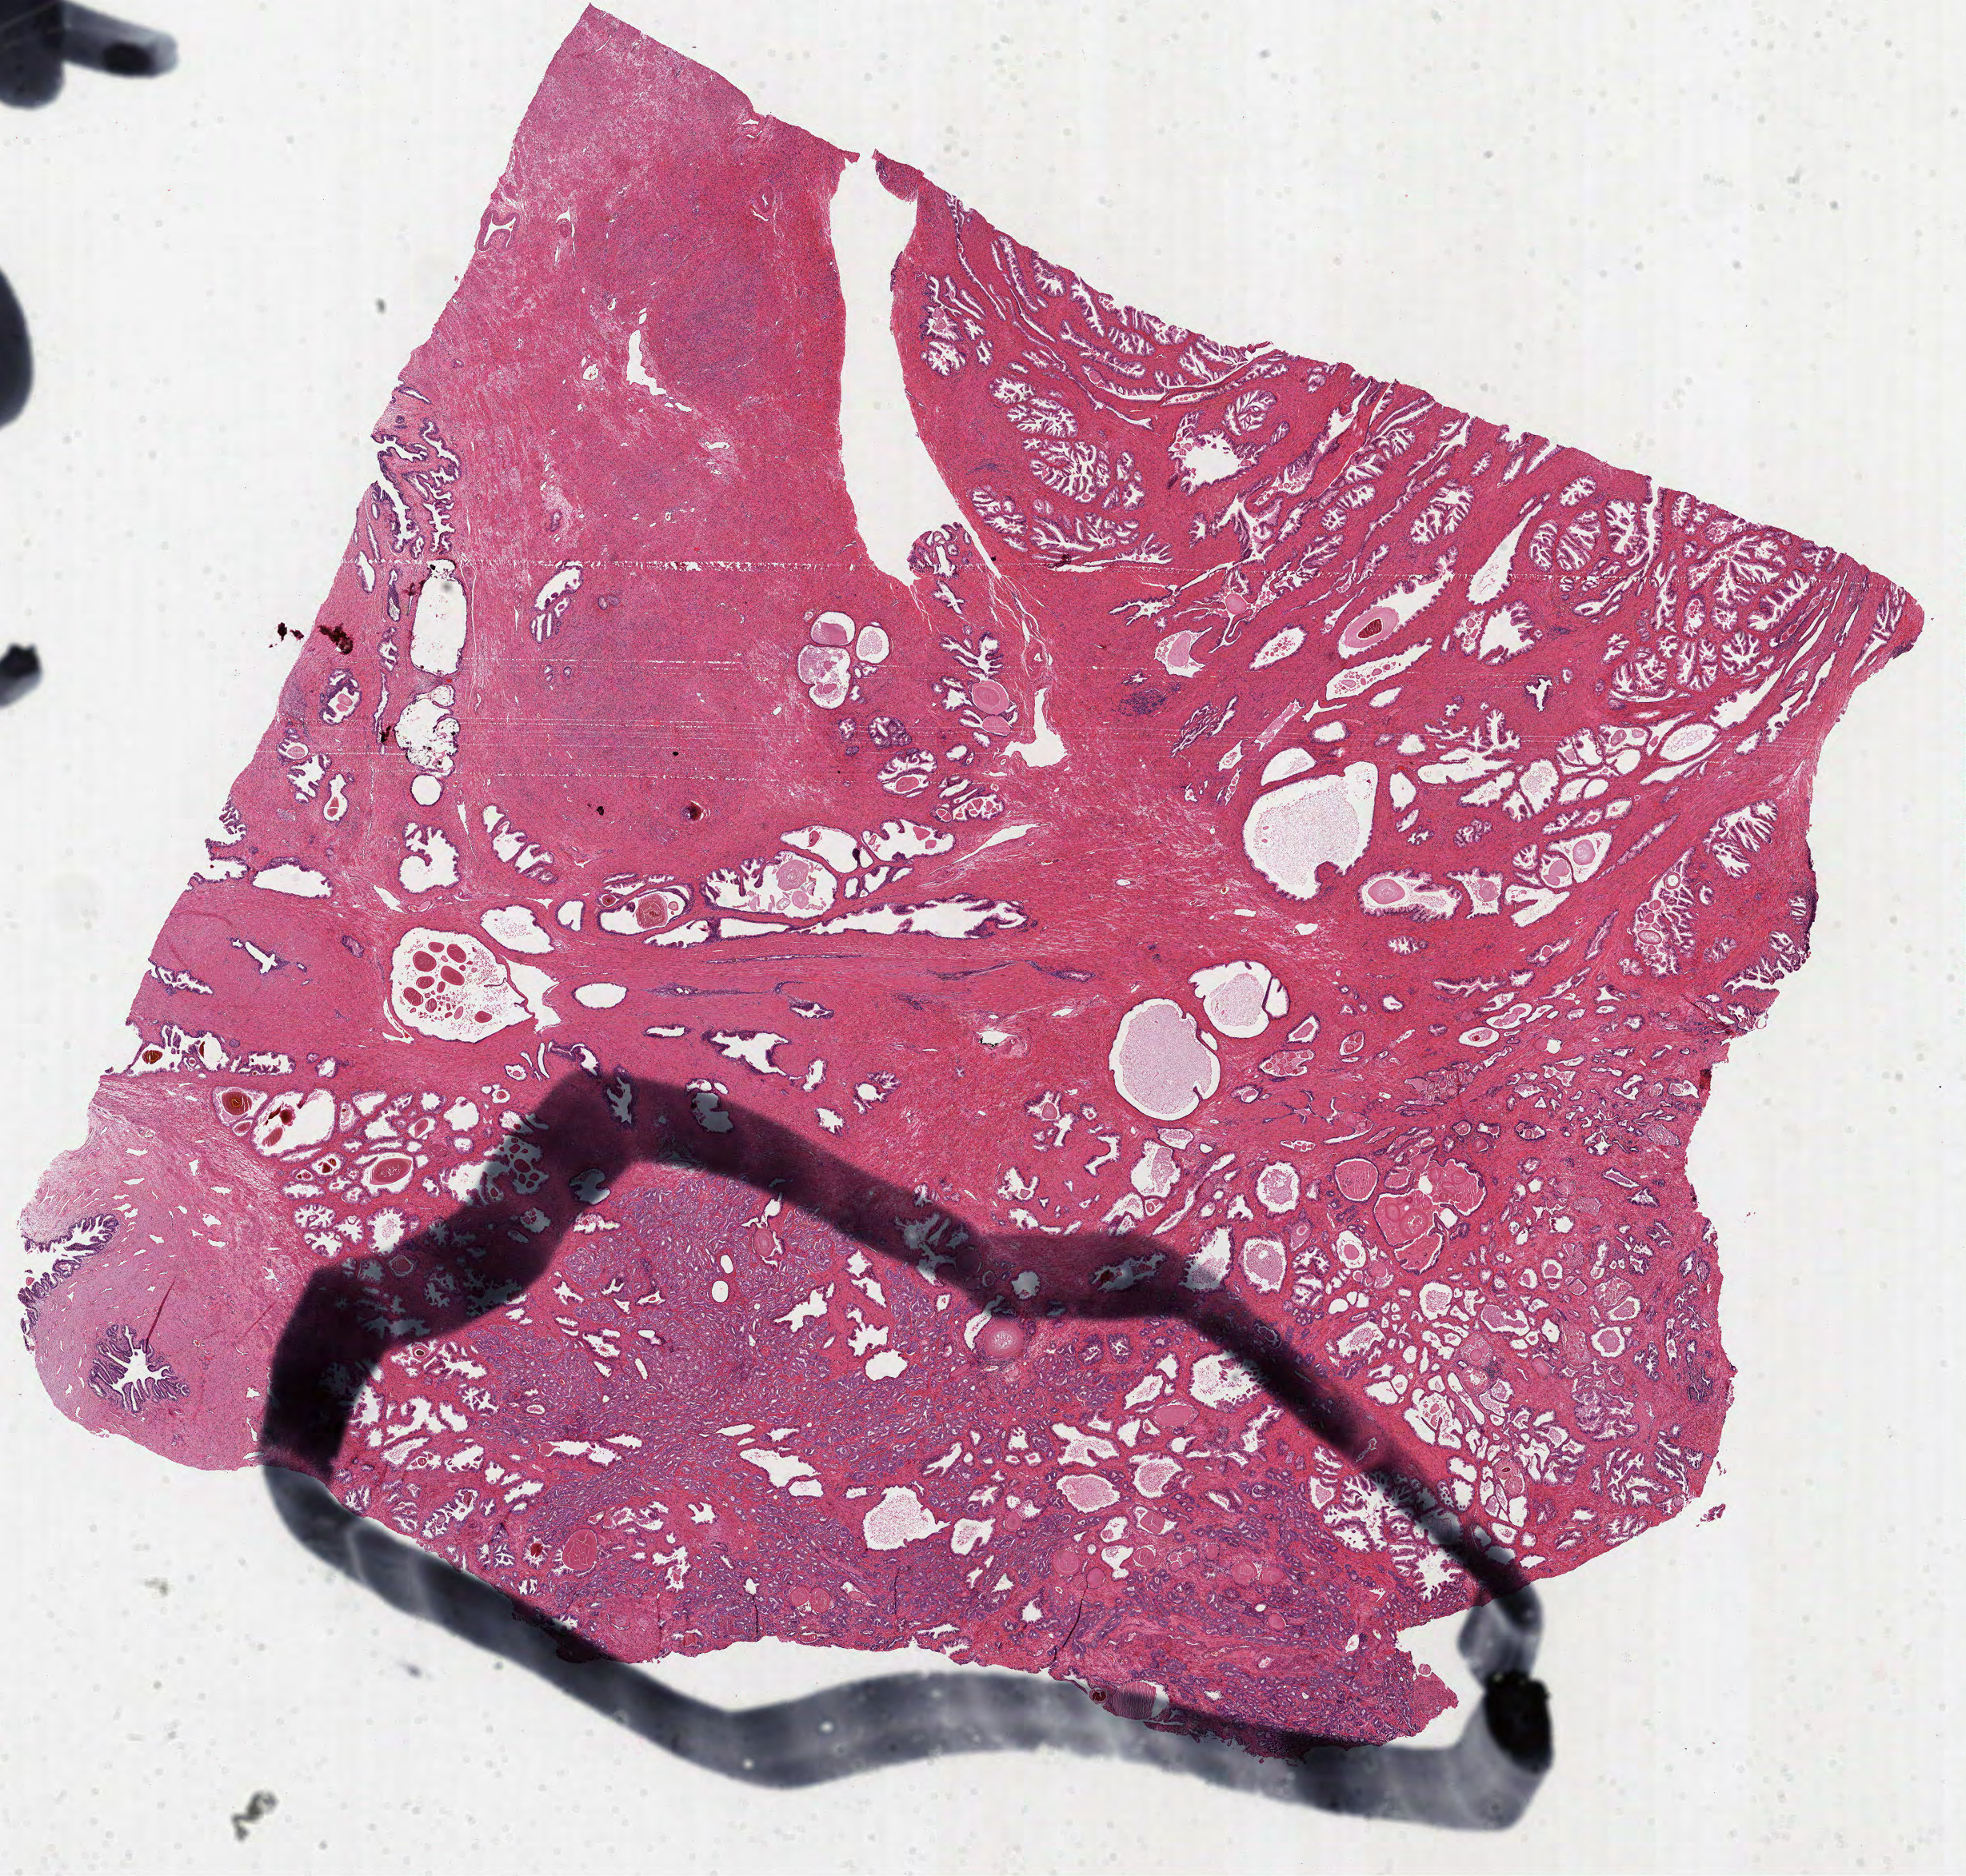
Hematoxylin and eosin (H&E) stained whole-slide image — whole scanned area (about 19.8 x 18.9 mm, slide scanned at 40x) shown as a low-resolution overview; formalin-fixed paraffin-embedded (FFPE) diagnostic section; sample: primary tumour, prostate. Patient: male, age at initial diagnosis 65 years. Gleason score: 7 (3+4).
• histologic diagnosis: Acinar cell carcinoma
• laterality: bilateral